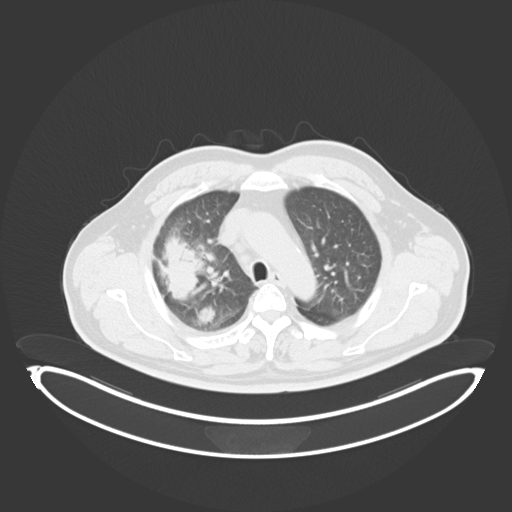
Chest CT, one axial slice; position 224 of 284 along the scan axis; reconstruction kernel B30f; lung window (W 1500 / L -600 HU); 3 mm slice thickness; 512 × 512 image matrix. Male patient, age 55 years. Case-level facts recorded for this patient, not image findings: clinical TNM (as recorded): T3 N2 M1.
Outlined on this slice (rectangle marked by the reading radiologist):
- lung tumour (recorded histology: adenocarcinoma): bounding box (x1, y1, x2, y2) in pixels: (158, 224, 205, 300)